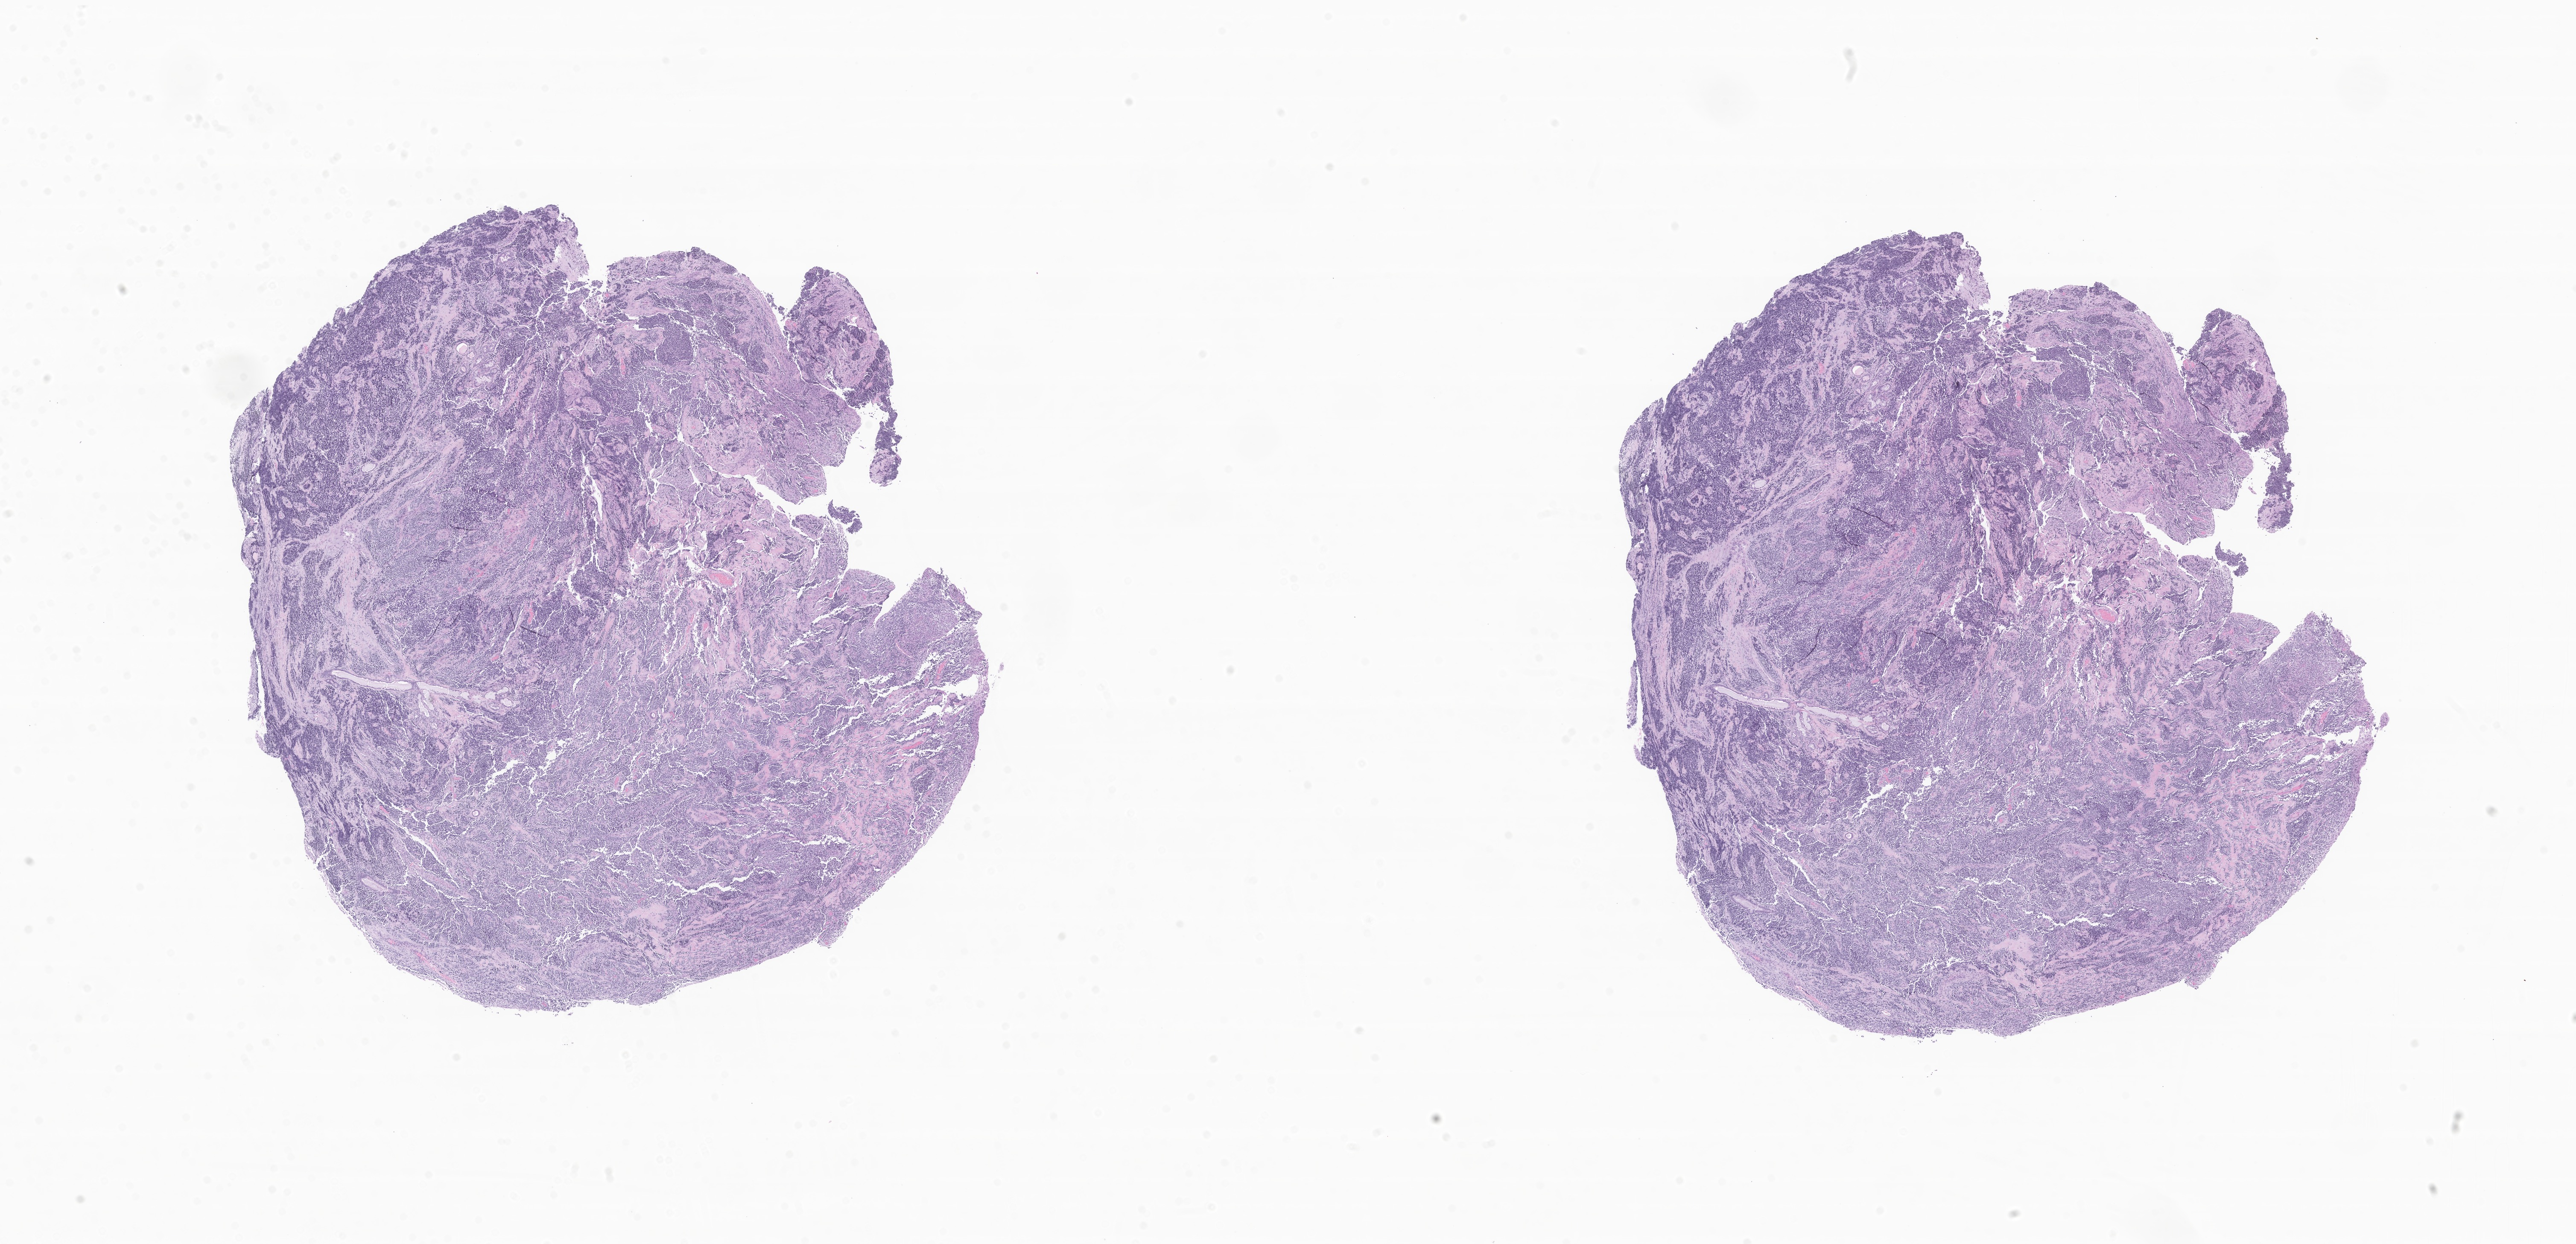
H&E whole-slide image of tumor tissue from the nasal sinus — whole scanned area (about 25.4 x 12.3 mm) shown as a low-resolution overview, FFPE section. Patient: male, age 241 months (20 years 1 month).
Diagnosis: Rhabdomyosarcoma, NOS.